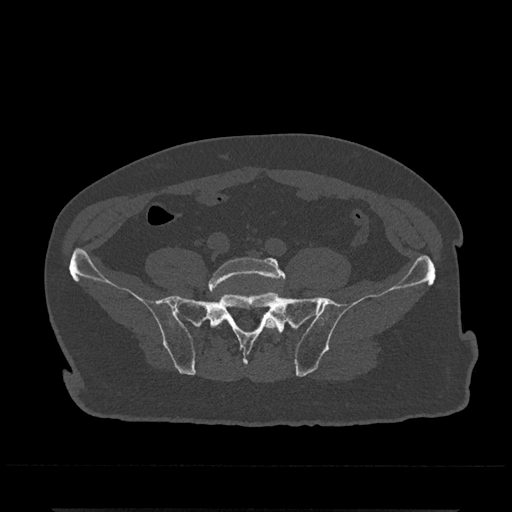
CT including the spine, one axial slice; position 47 of 797 along the scan axis; 120 kVp; bone window (W 1800 / L 400 HU); 512 × 512 image matrix. Patient: male, 67 years. Case-level facts recorded for this patient, not image findings: primary cancer: prostate.
Annotated regions visible in this slice (semi-automatically segmented with operator editing):
- L5 vertebra: bounding box <208,257,285,330> (left, top, right, bottom; pixels)